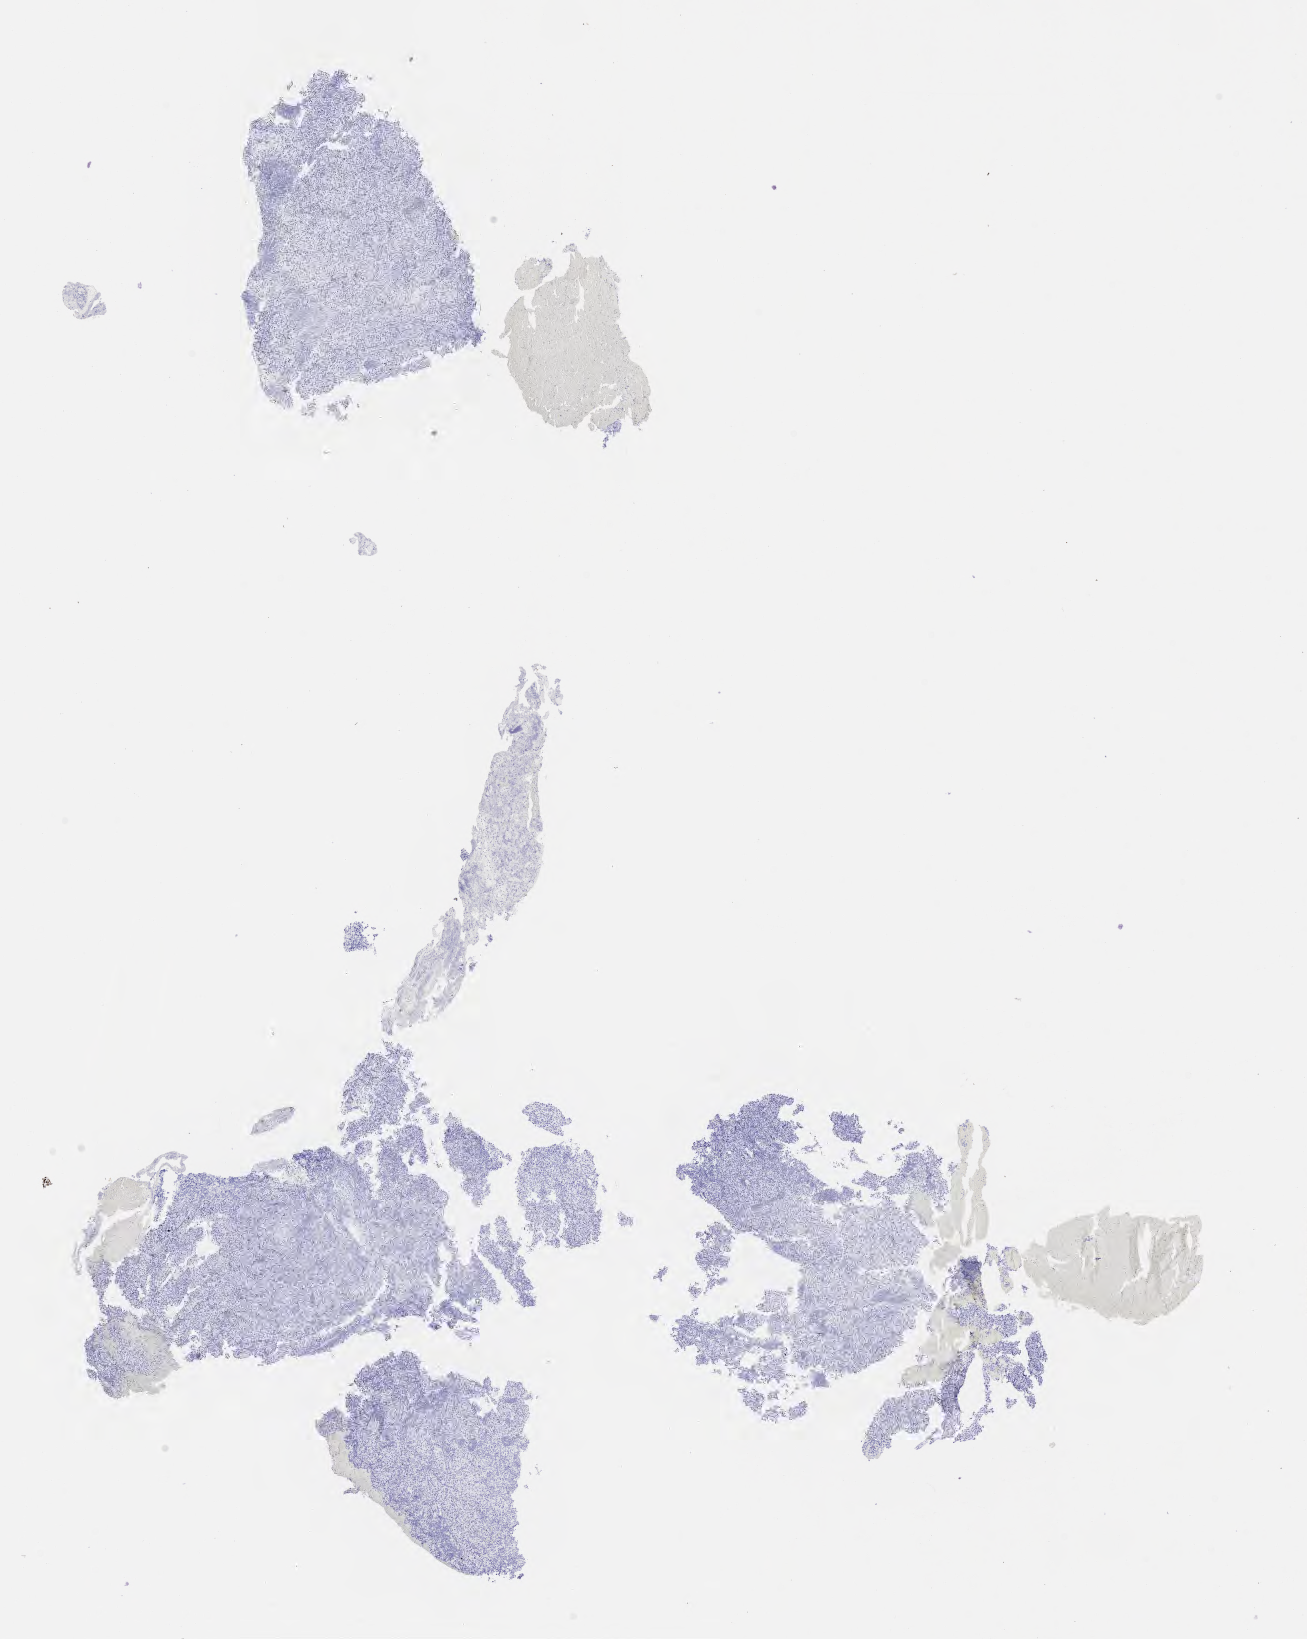
Immunohistochemistry (IHC) whole-slide image stained for p40, a low-resolution overview of the entire scanned area, about 10.6 x 13.3 mm; tumor tissue; anatomic site: cervix. Patient: female, 33 years old.
Diagnosis: Squamous cell carcinoma, large cell, nonkeratinizing, NOS.